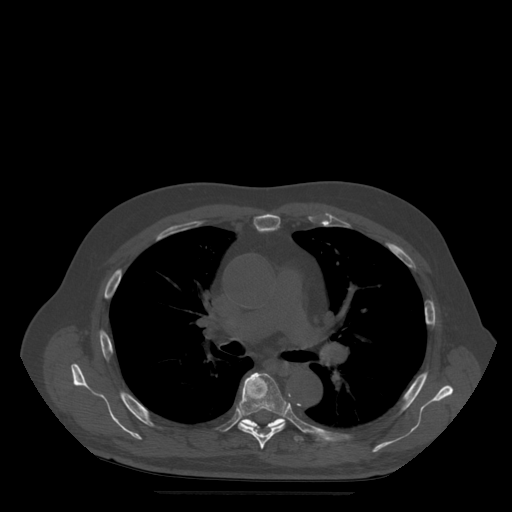
CT including the spine, one axial slice. Slice 348 of 522 in the series (ordered by position). Bone window (W 1800 / L 400 HU). 1.25 mm slice thickness. 512 × 512 image matrix, field of view 420 × 420 mm. Patient age 72 years. From the clinical record (not read from this slice): primary cancer: prostate.
Outlined on this slice (semi-automatically segmented with operator editing):
- T6 vertebra: bounding box [x1, y1, x2, y2] px = [238, 373, 288, 449]
- T7 vertebra: [243, 419, 303, 441]